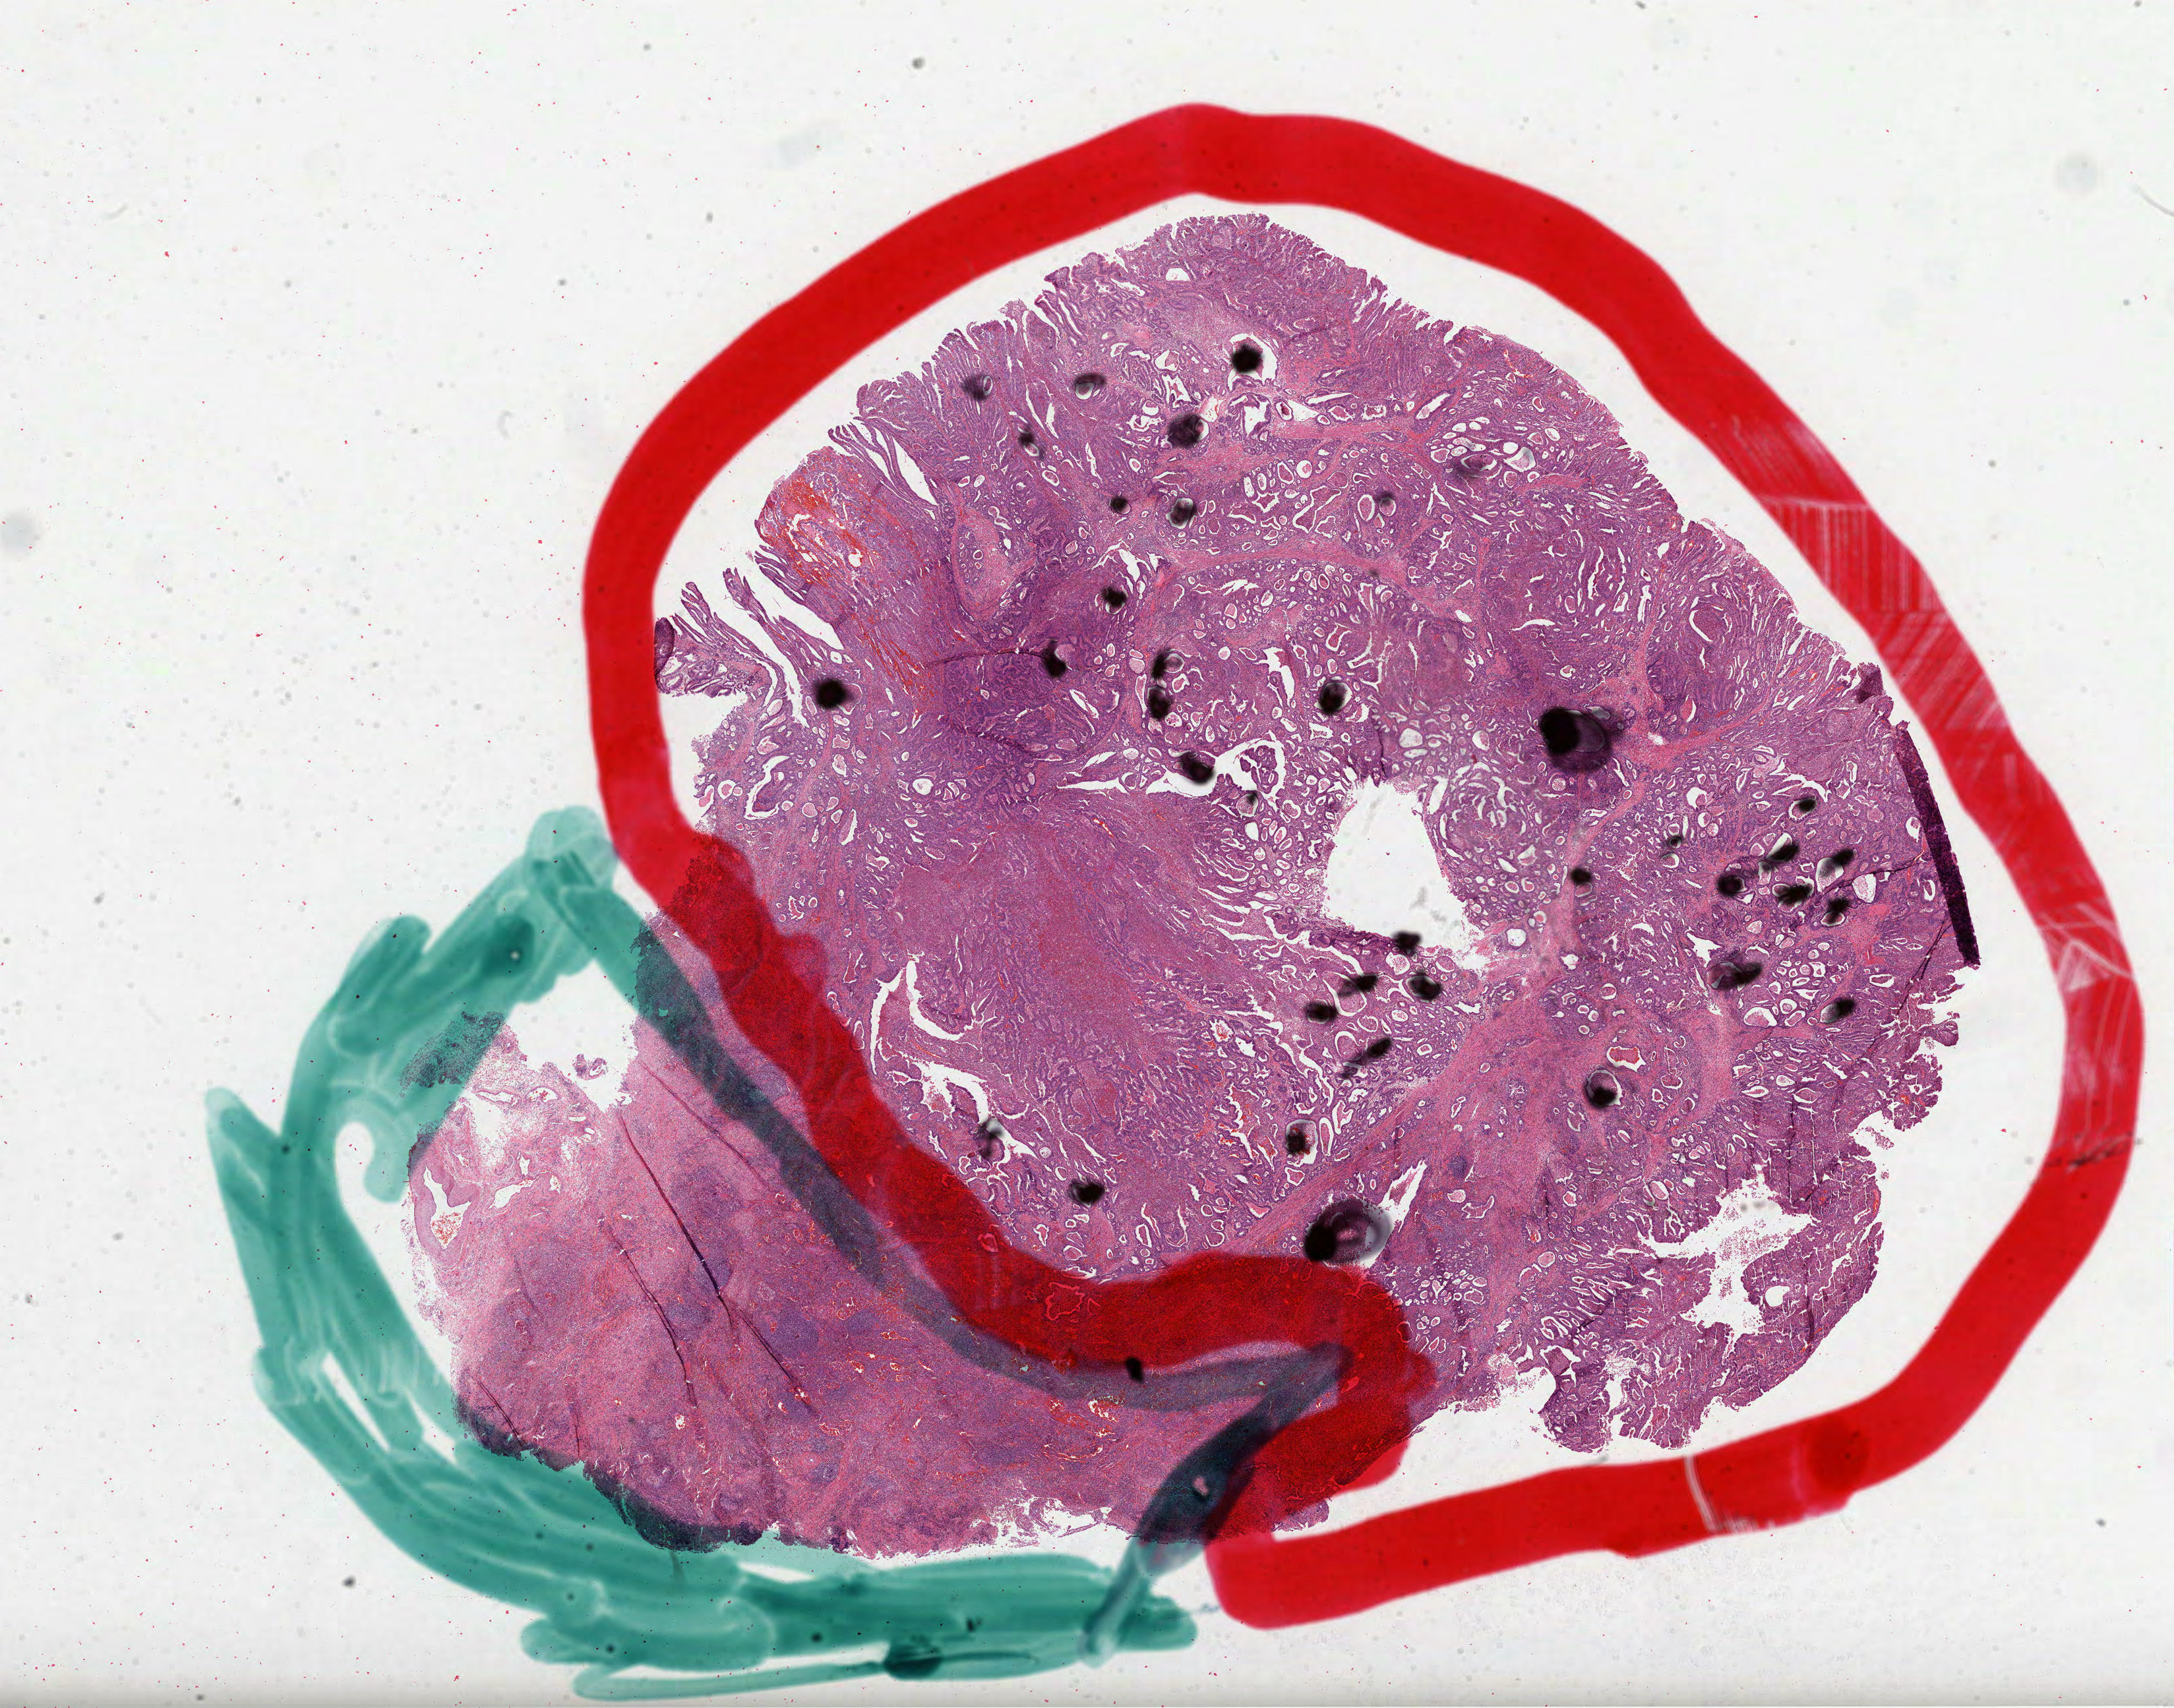
H&E whole-slide image — shown as a low-resolution overview of the whole scanned area (about 26.6 x 20.9 mm, acquisition: 40x scan), formalin-fixed paraffin-embedded (FFPE) diagnostic section, sample: primary tumour, stomach. Male patient; age at initial diagnosis 41 years. Histologic grade: G2 (moderately differentiated).
Histologic diagnosis: Adenocarcinoma, NOS (cardia, NOS). Lymph nodes positive (case pathology): 0 of 15 examined. TNM: T2 N0 M0. AJCC pathologic stage: IB (7th edition).